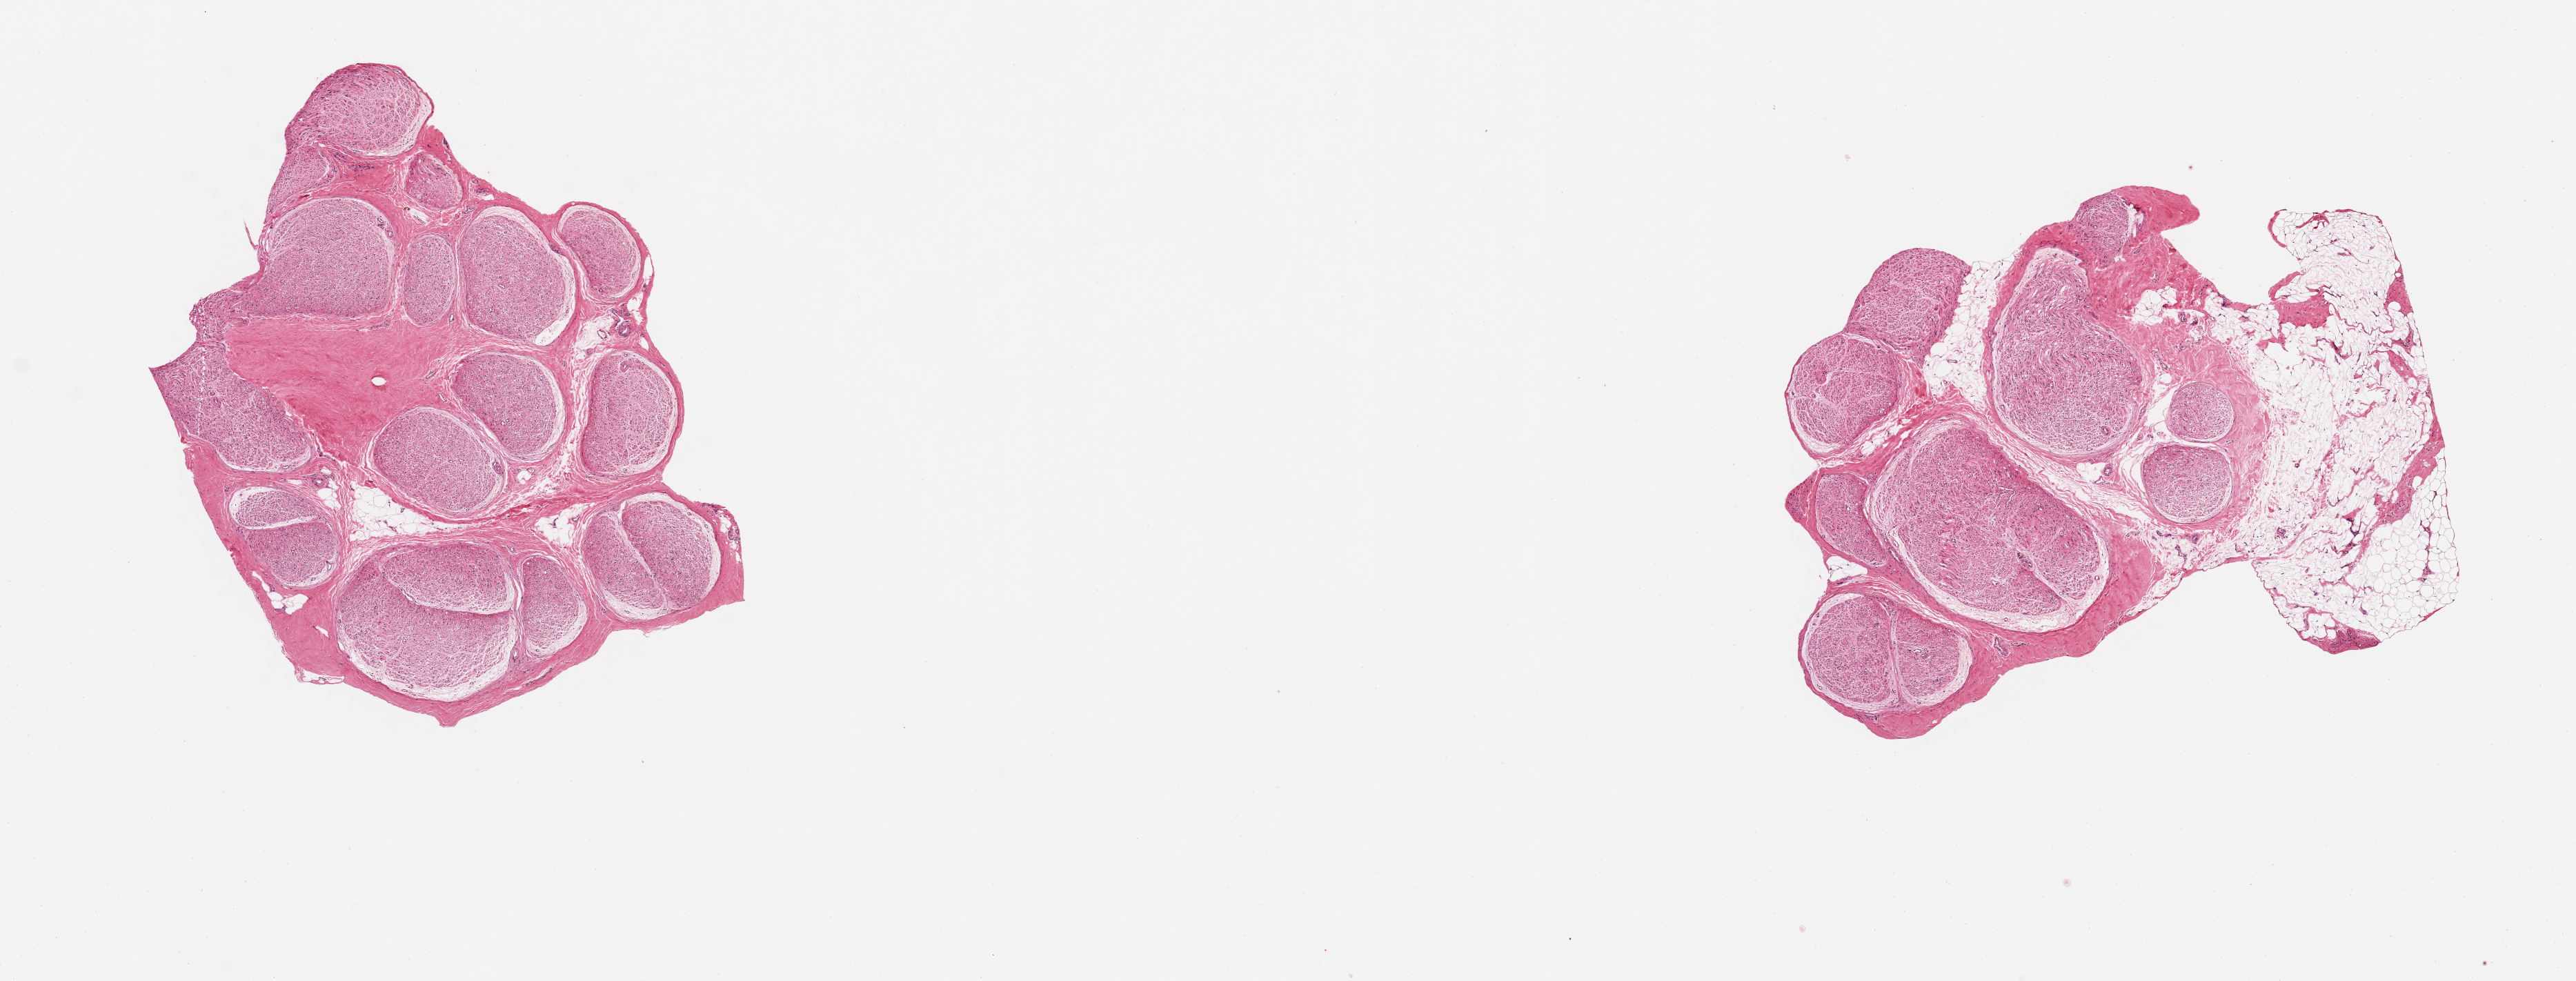
Whole-slide image, hematoxylin and eosin (H&E) stain, brightfield — low-resolution overview of the scanned area, about 14.8 x 5.6 mm (slide scanned at 20x).
Specimen: PAXgene-fixed paraffin-embedded (PFPE) section; target tissue: tibial nerve; donor tissue sample.